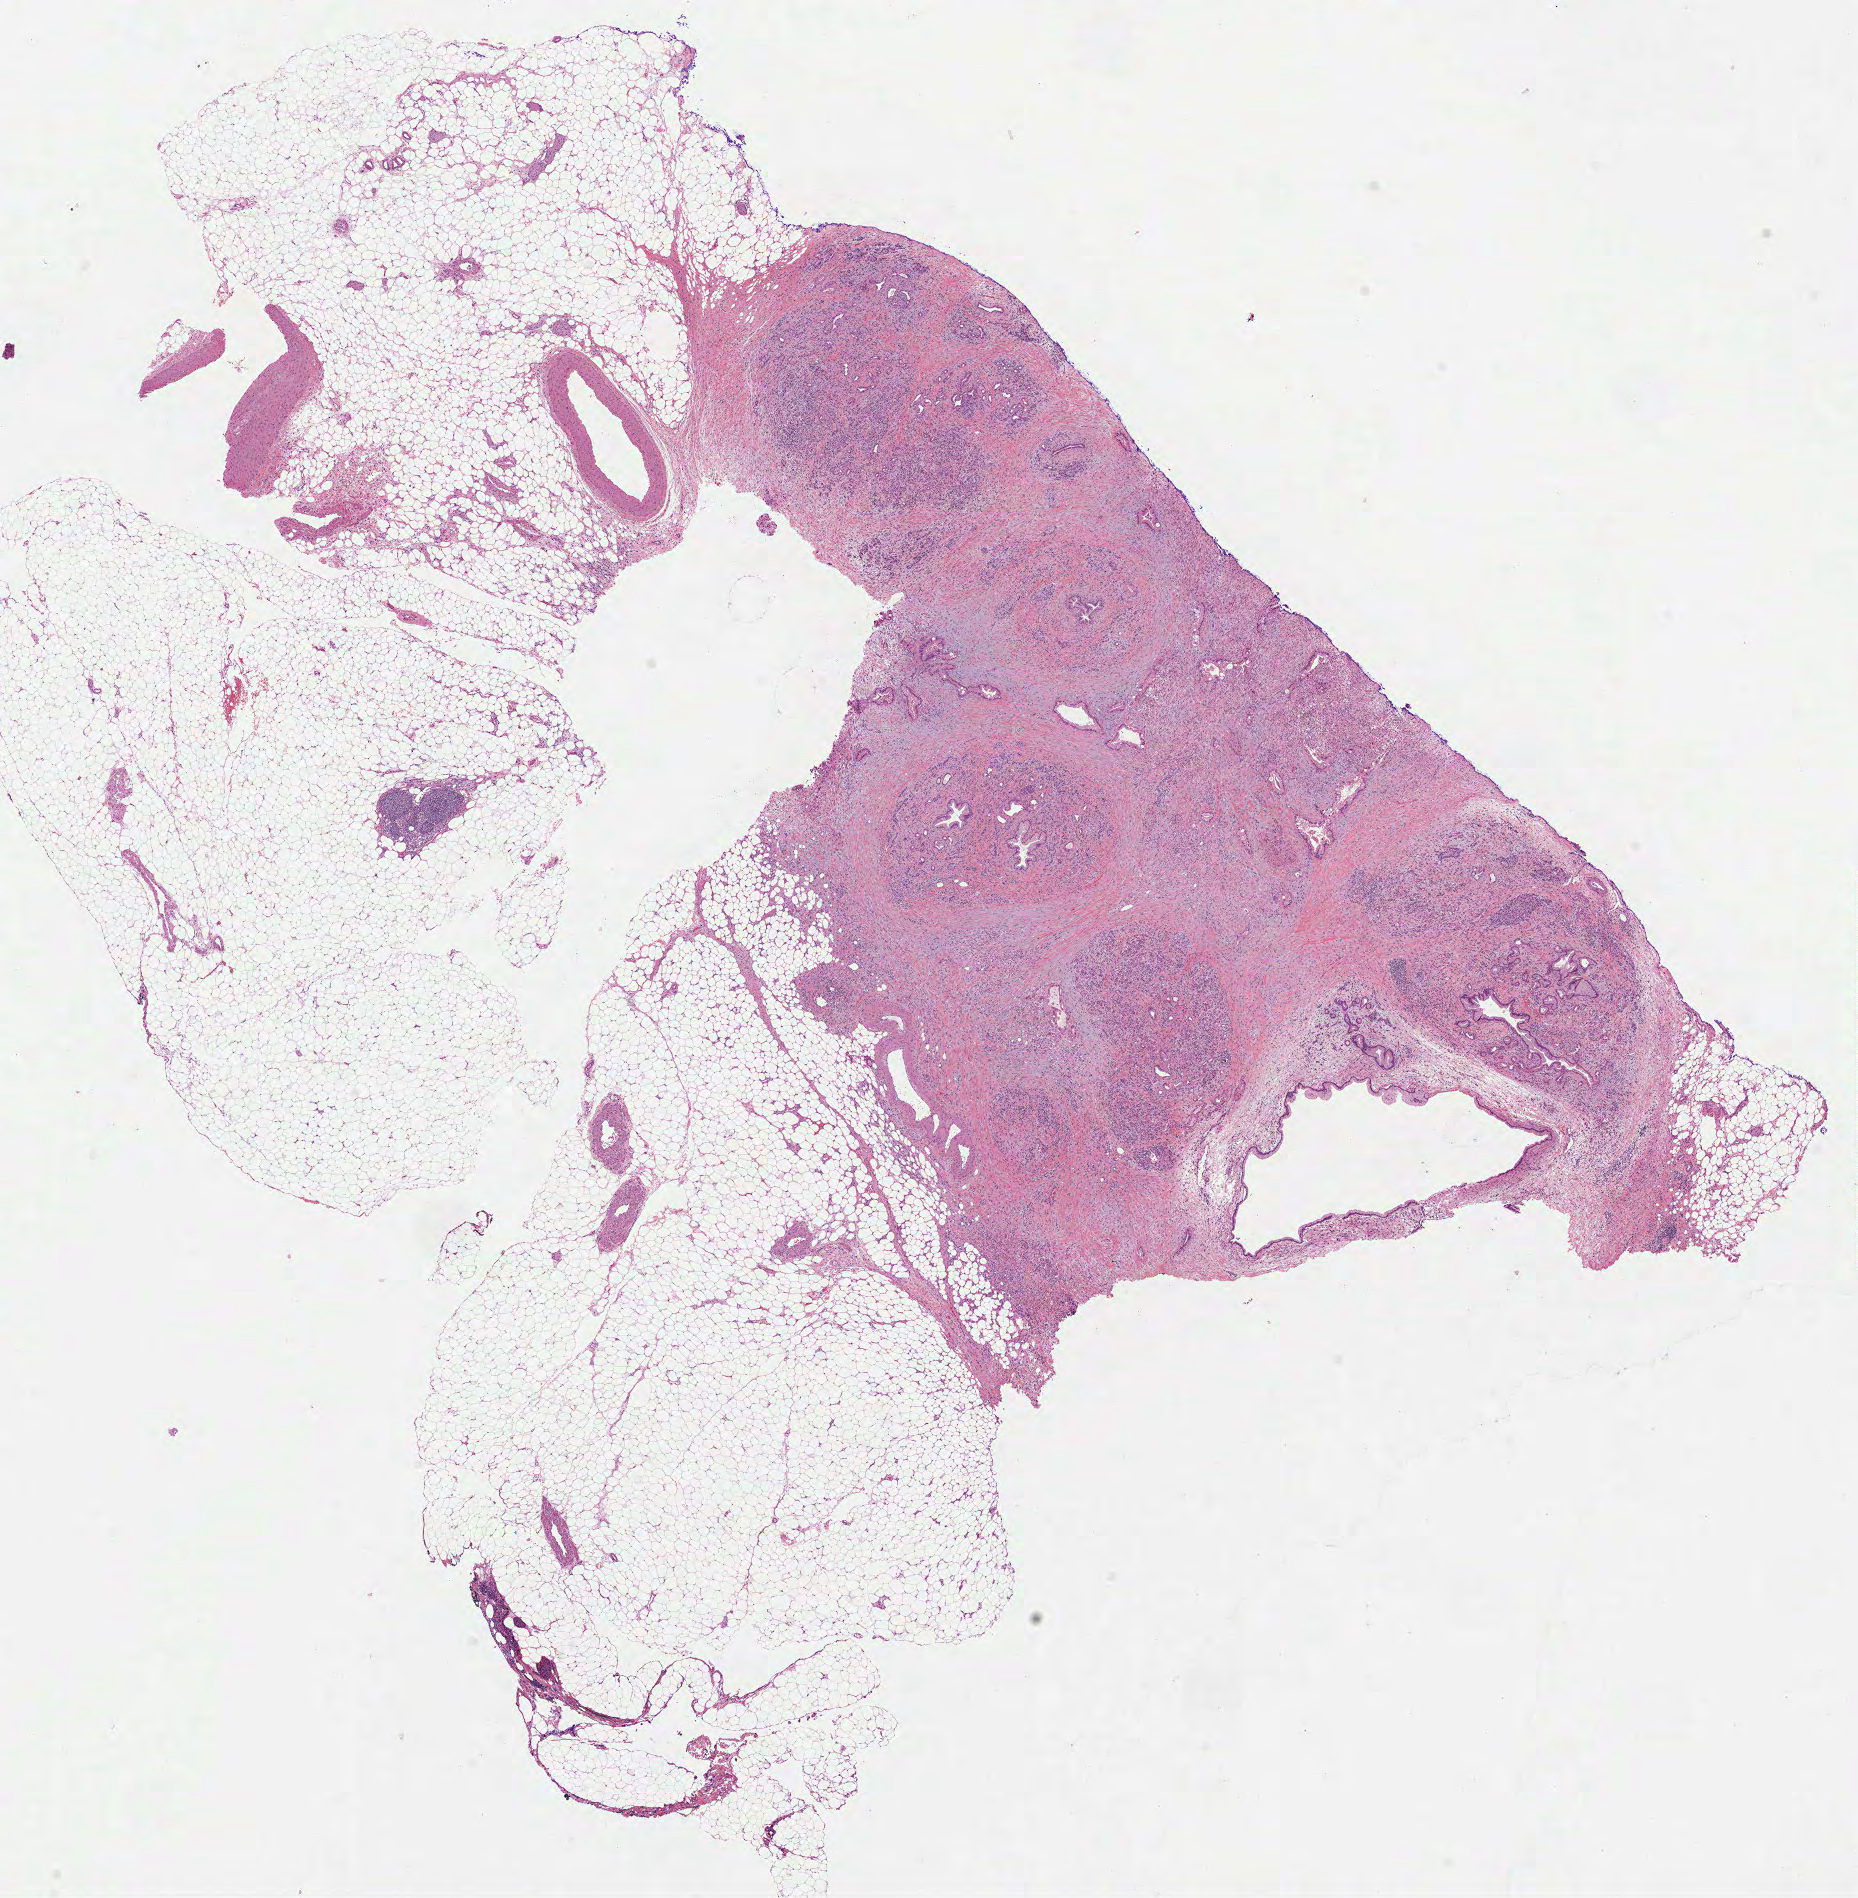
Whole-slide histology image, Hematoxylin and eosin (H&E) stained — shown as a low-resolution overview of the whole scanned area (about 15.0 x 15.3 mm); formalin-fixed paraffin-embedded (FFPE) diagnostic section; sample: primary tumour, pancreas. Male, age 65 years at initial diagnosis. Histologic grade: G2 (moderately differentiated).
Lymph nodes positive (case pathology): 0 of 17 examined. AJCC pathologic stage: IIA (7th edition). Diagnosis: Infiltrating duct carcinoma, NOS.